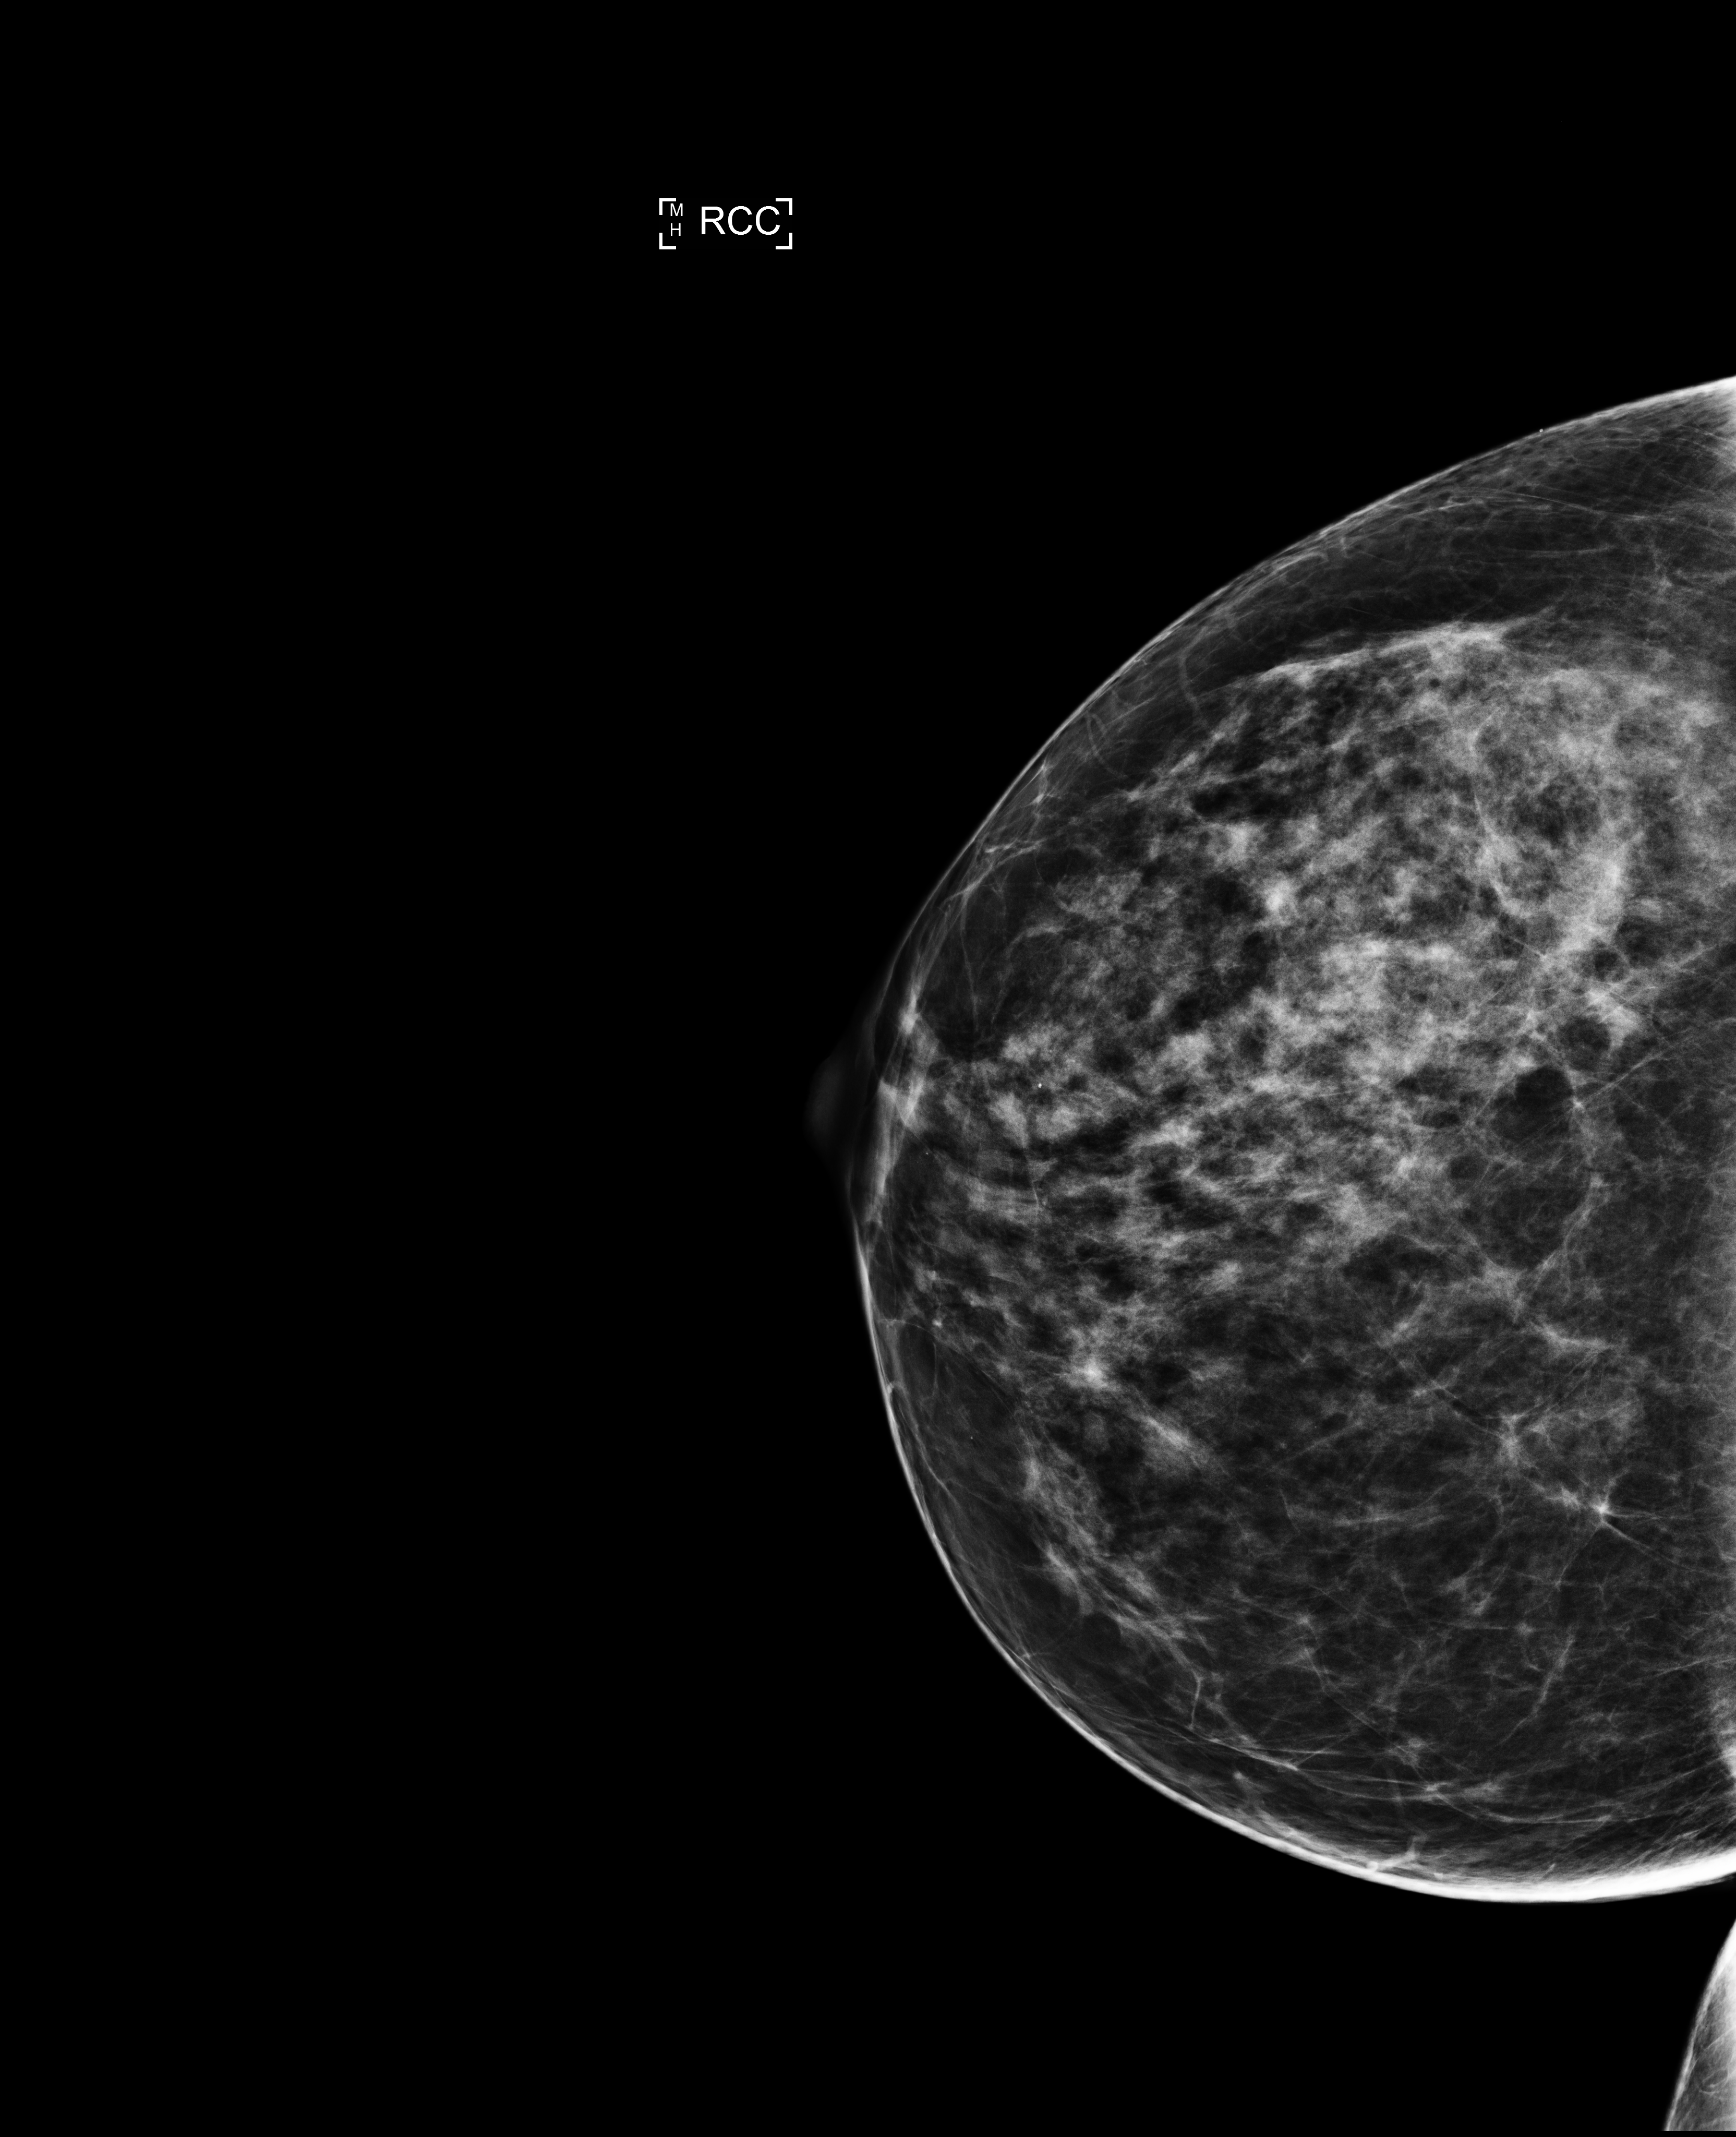
Annual screening mammography examination, compressed breast thickness 71 mm. Patient aged 48 years (female).
Image type: full-field digital mammogram. Breast: right. Projection: CC view.